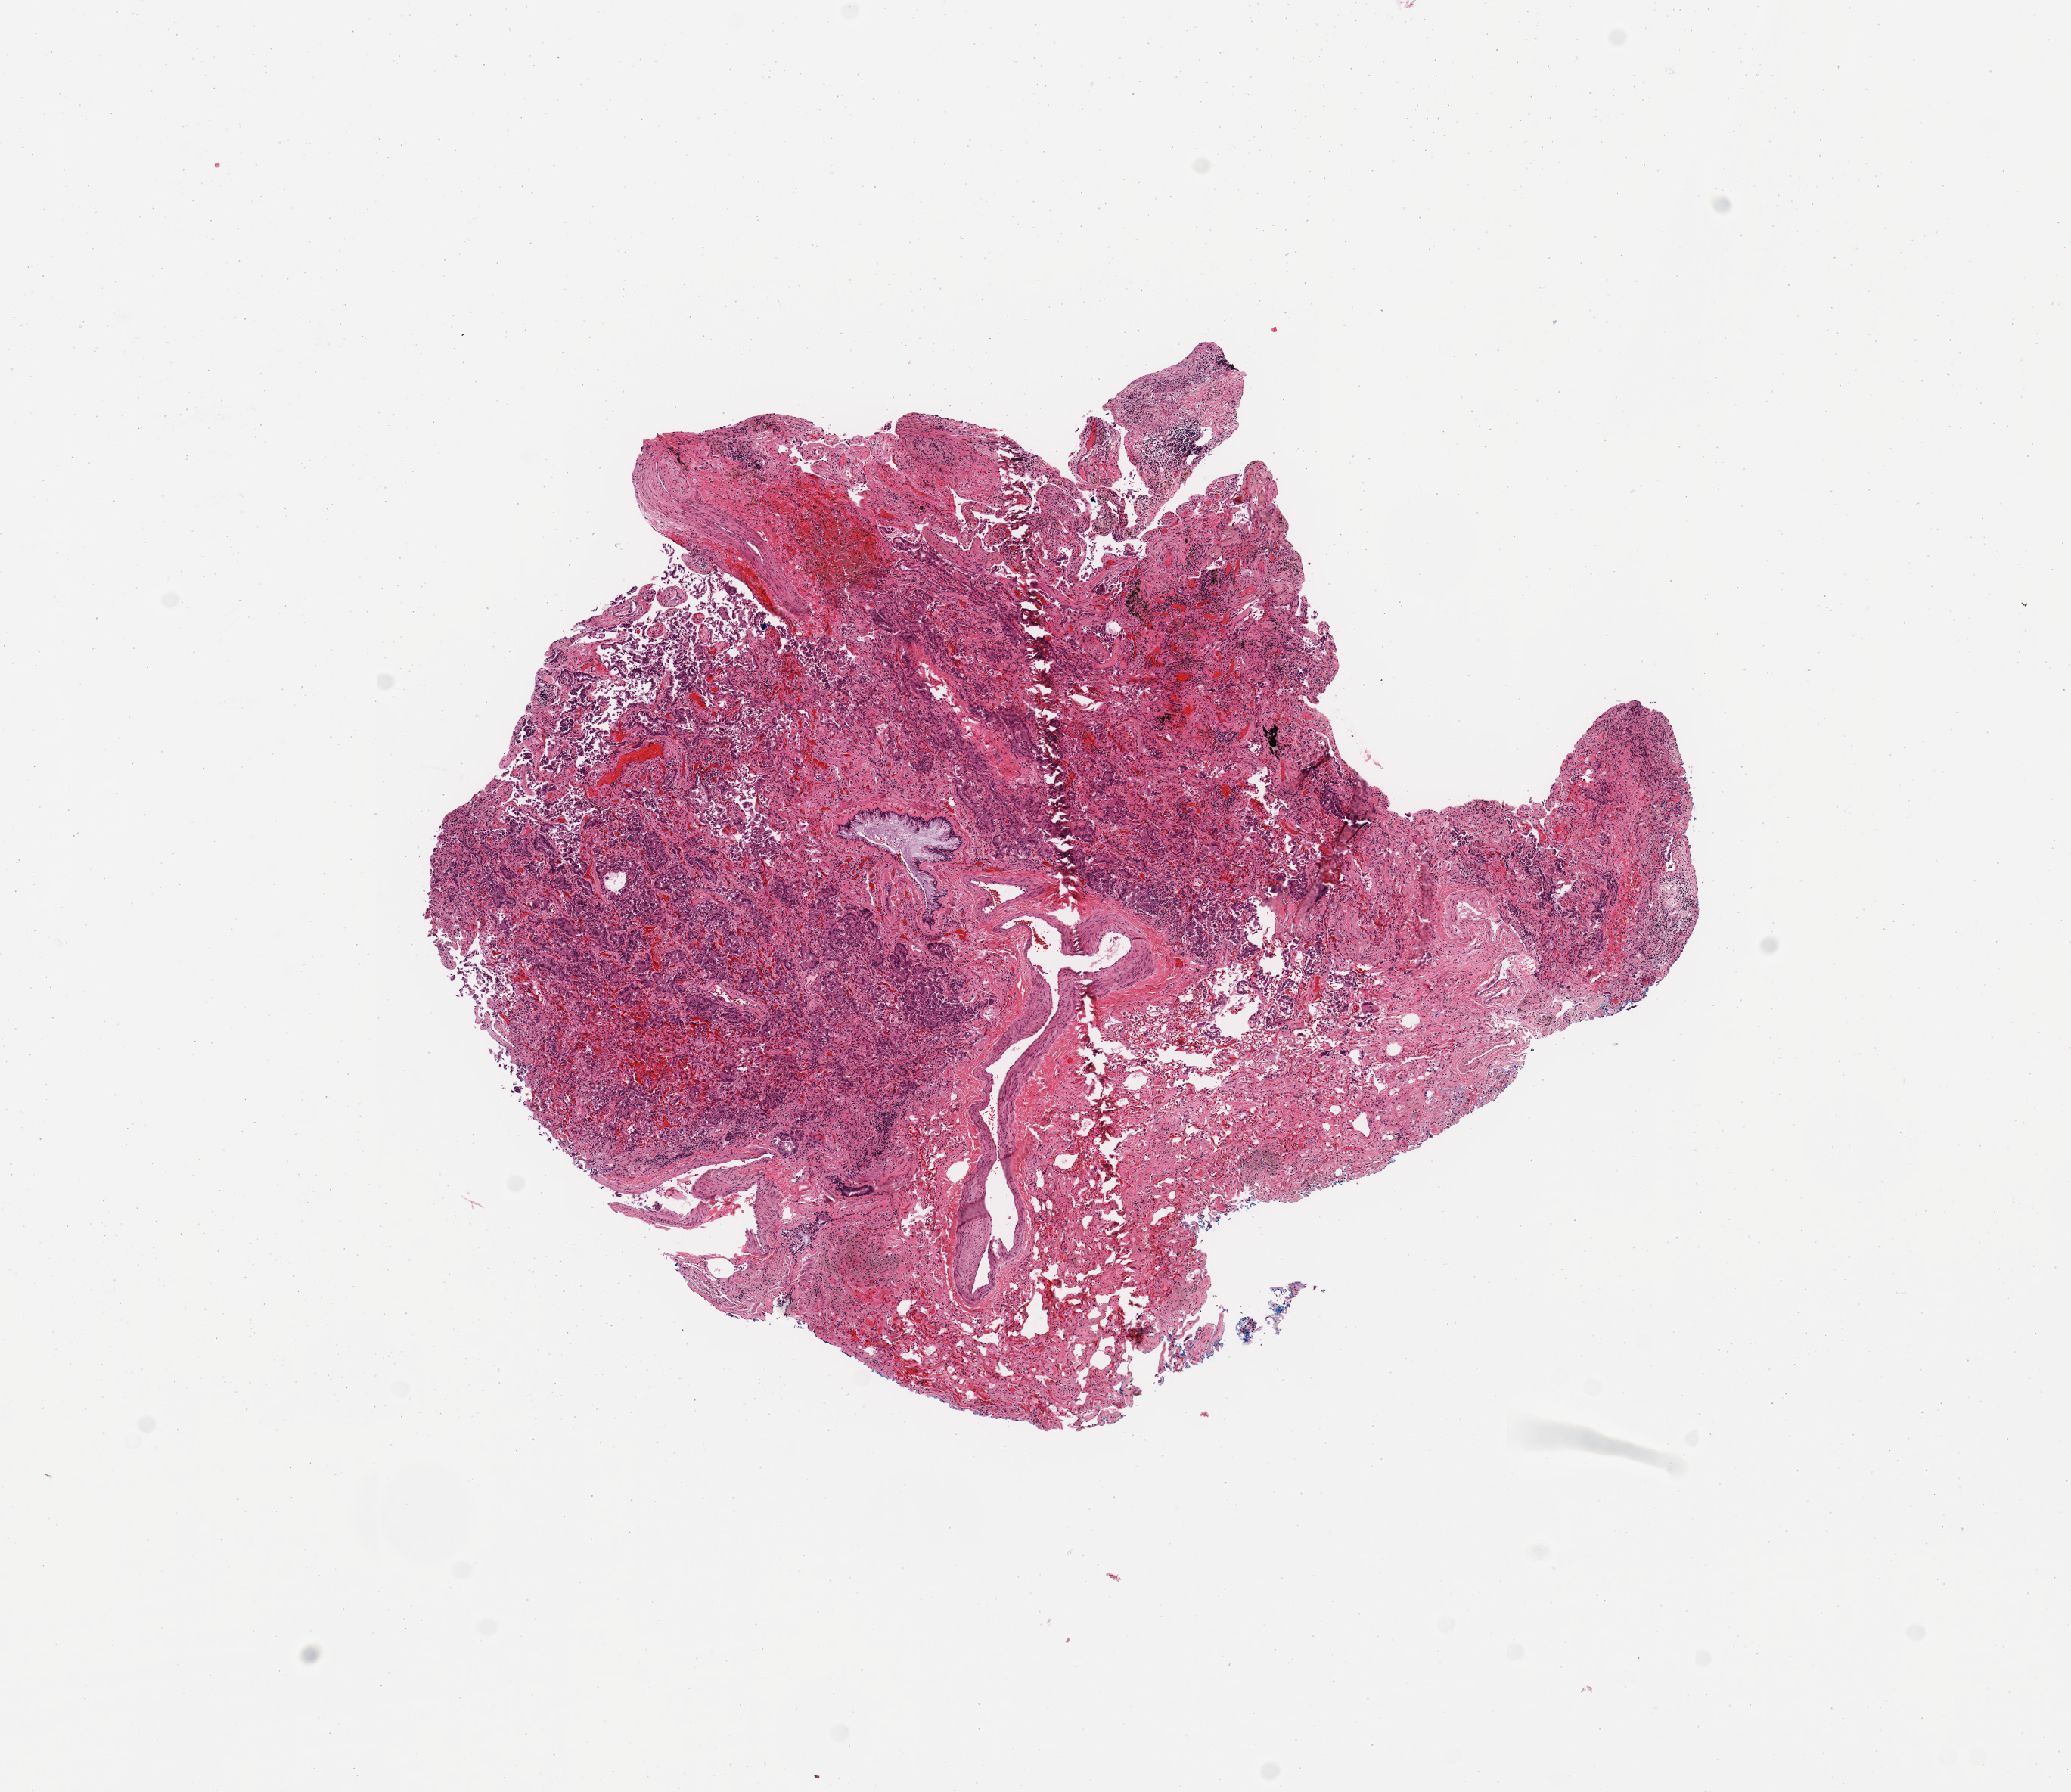
H&E-stained whole-slide image — a low-resolution overview of the entire scanned area, about 10.8 x 9.4 mm (slide scanned at 20x). Tumour tissue sample, sampled site: lung. Female, 58 y/o. Histologic grade: G1 (well differentiated). Slide review estimates, as recorded: tumour nuclei 60%, necrosis 2%.
Histologic diagnosis: Adenocarcinoma, NOS. AJCC pathologic stage: IA. Primary tumour site (as recorded): left upper lobe.